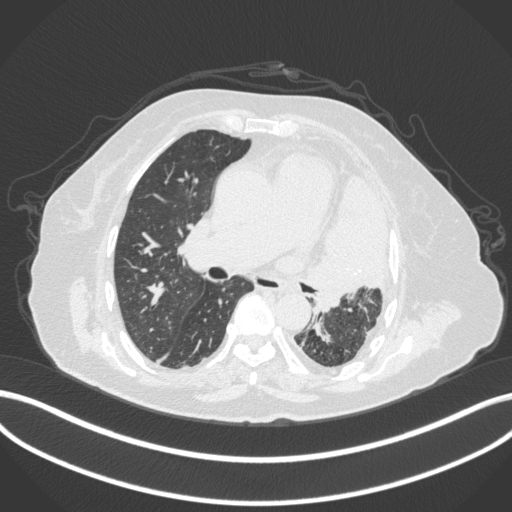
Chest CT, one axial slice; reconstruction kernel B31f; 120 kVp; lung window (W 1500 / L -600 HU); 1 mm slice thickness; 512 × 512 image matrix, field of view 400 × 400 mm. Female patient, age 75 years. Case-level facts recorded for this patient, not image findings: clinical TNM (as recorded): T3 N3 M1.
Outlined on this slice (bounding box drawn by a radiologist):
- lung tumour (recorded histology: adenocarcinoma): bounding box <312,171,395,315> (left, top, right, bottom; pixels)